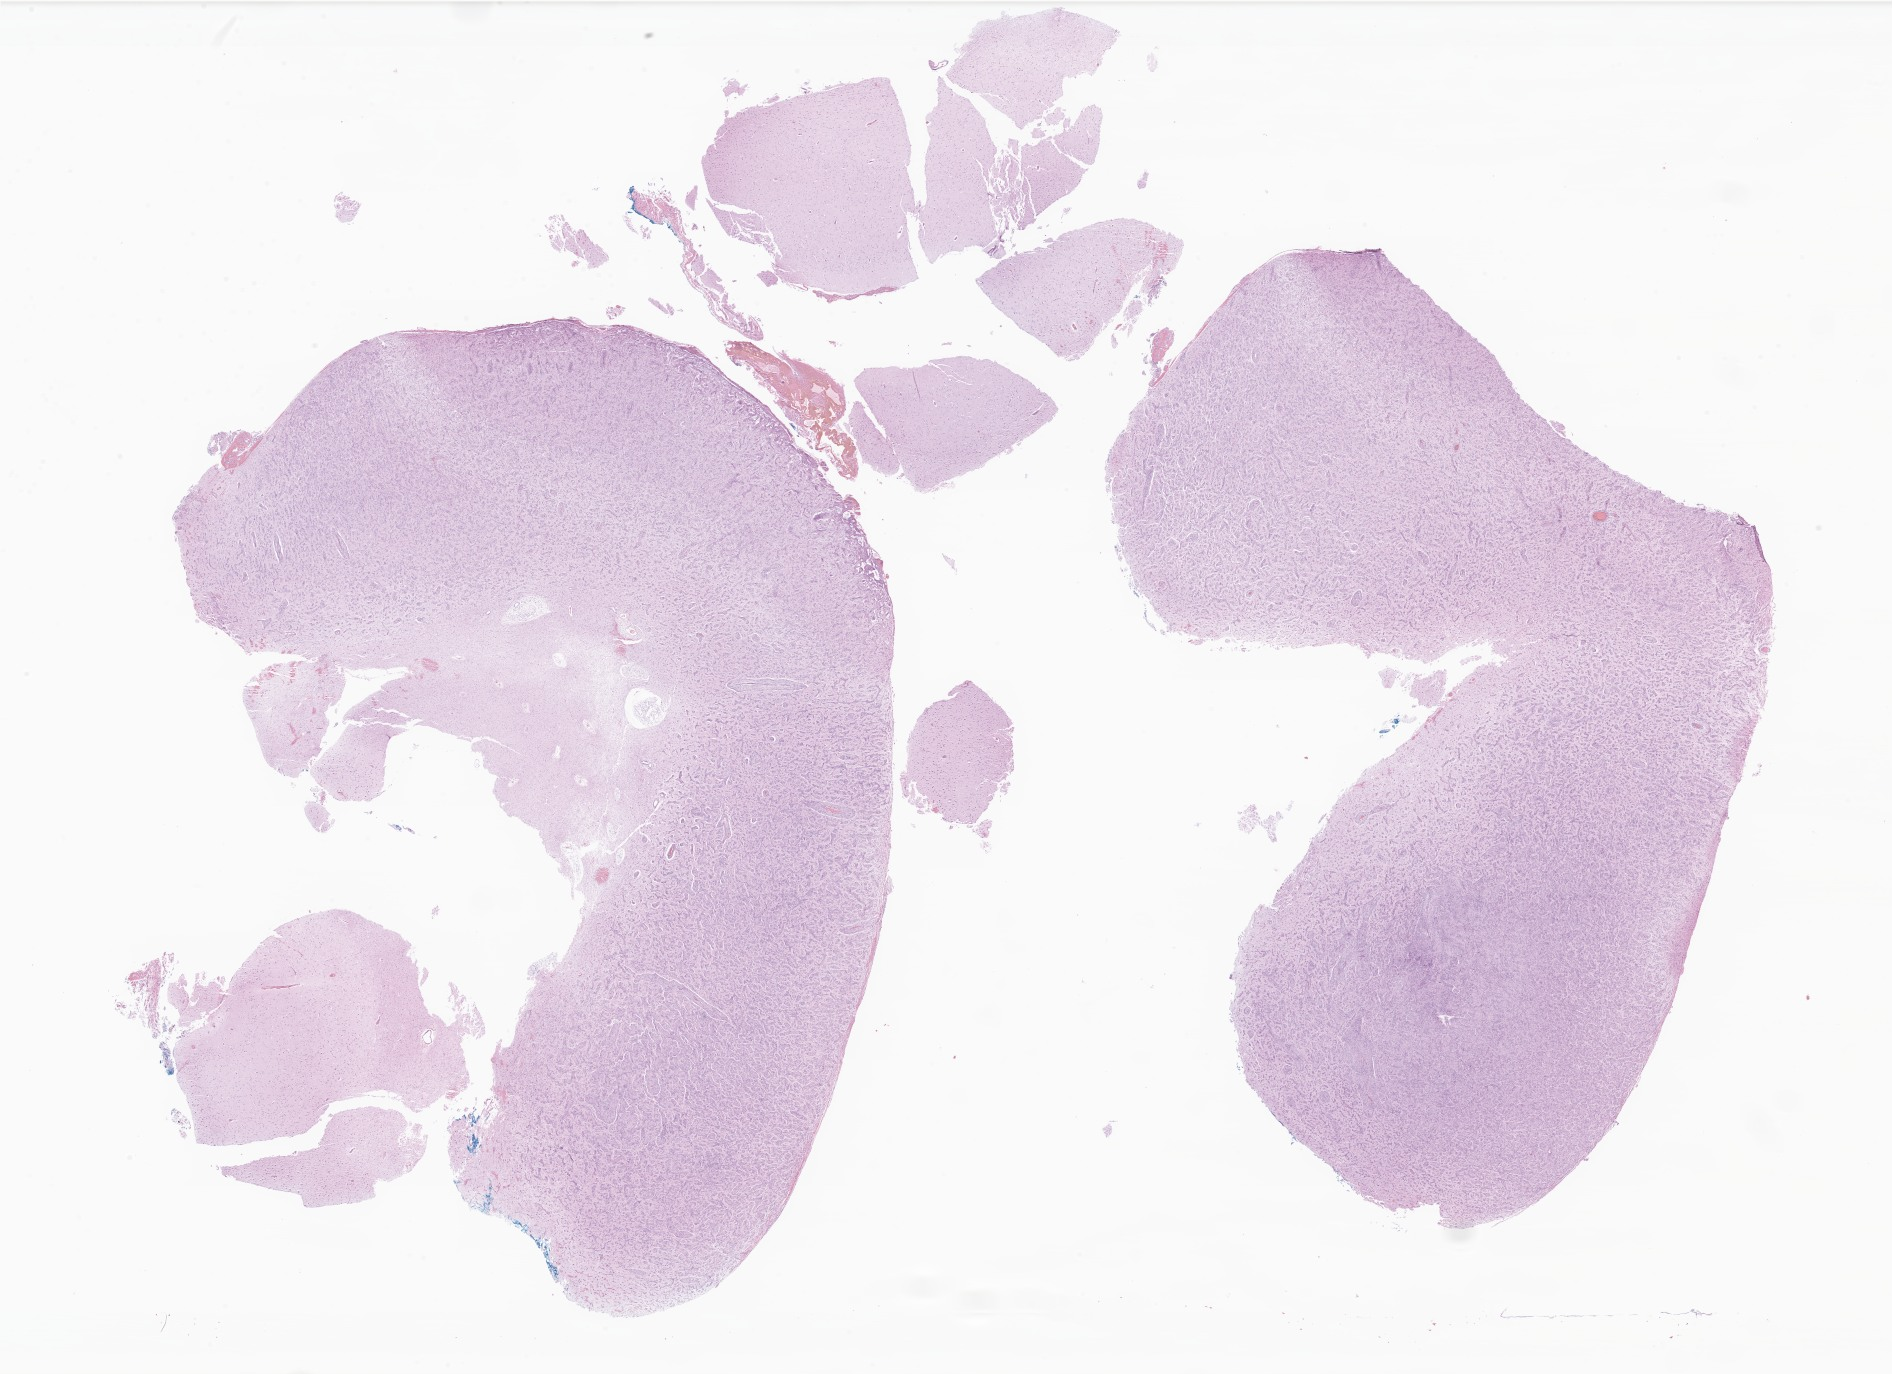
H&E whole-slide image of tumor tissue from the brain, a low-resolution overview of the entire scanned area, about 31.9 x 23.2 mm; formalin-fixed paraffin-embedded section. Patient female; age 44 months (3 years 8 months).
- diagnosis (ICD-O-3 morphology term): Neoplasm, benign